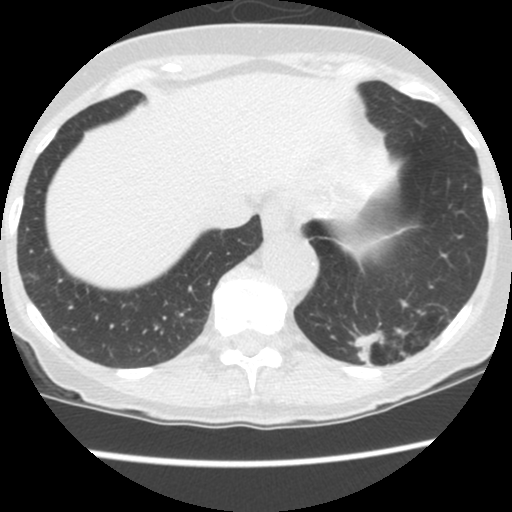
Low-dose screening chest CT, one axial slice. Position 29 of 130 along the scan axis. 120 kVp. Lung window (W 1500 / L -600 HU). 2.5 mm slice thickness. 512 × 512 image matrix, field of view 290 × 290 mm.
Annotated regions visible in this slice (outlined manually by an expert reader):
- lesion 1 (tumor, lower lobe of left lung): bounding box (x1, y1, x2, y2) in pixels: (353, 326, 383, 367)